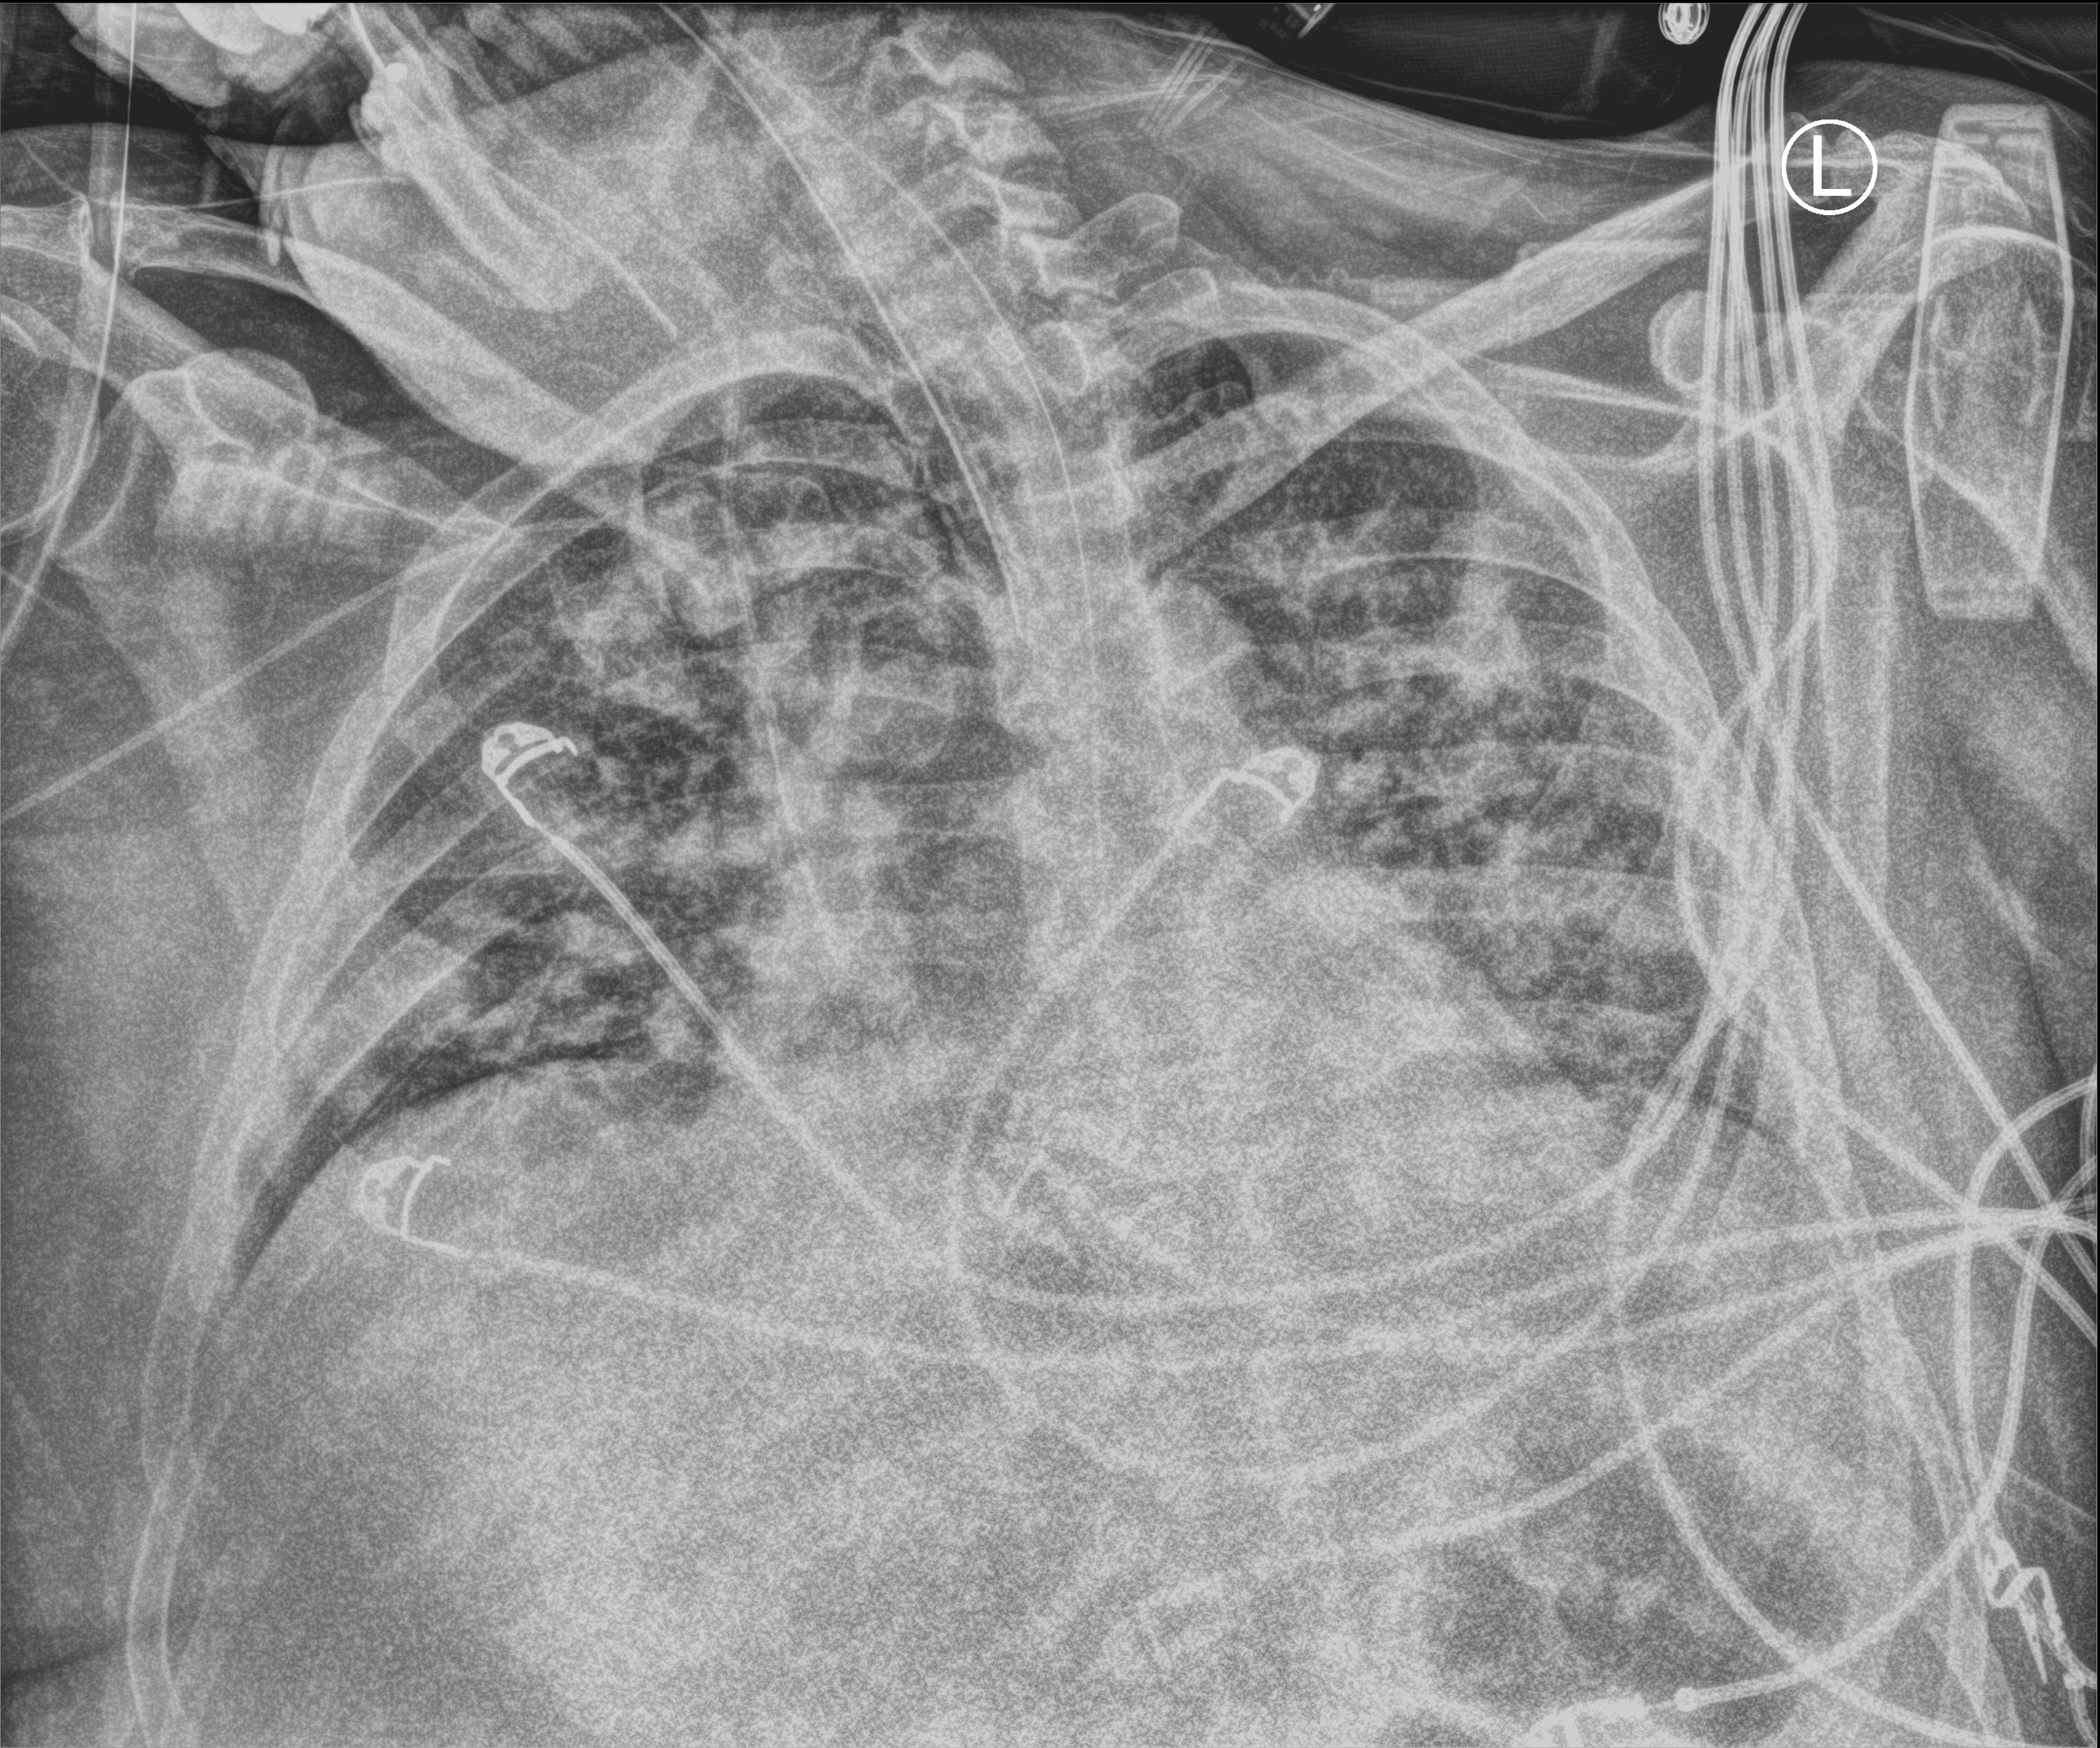
Bedside chest radiograph (computed radiography), anteroposterior (AP) projection. Male patient hospitalised with COVID-19, age 18–59 years.
Admission-level facts for this patient (not findings on this image; timing relative to this image not recorded):
- smoking status (admission record): former